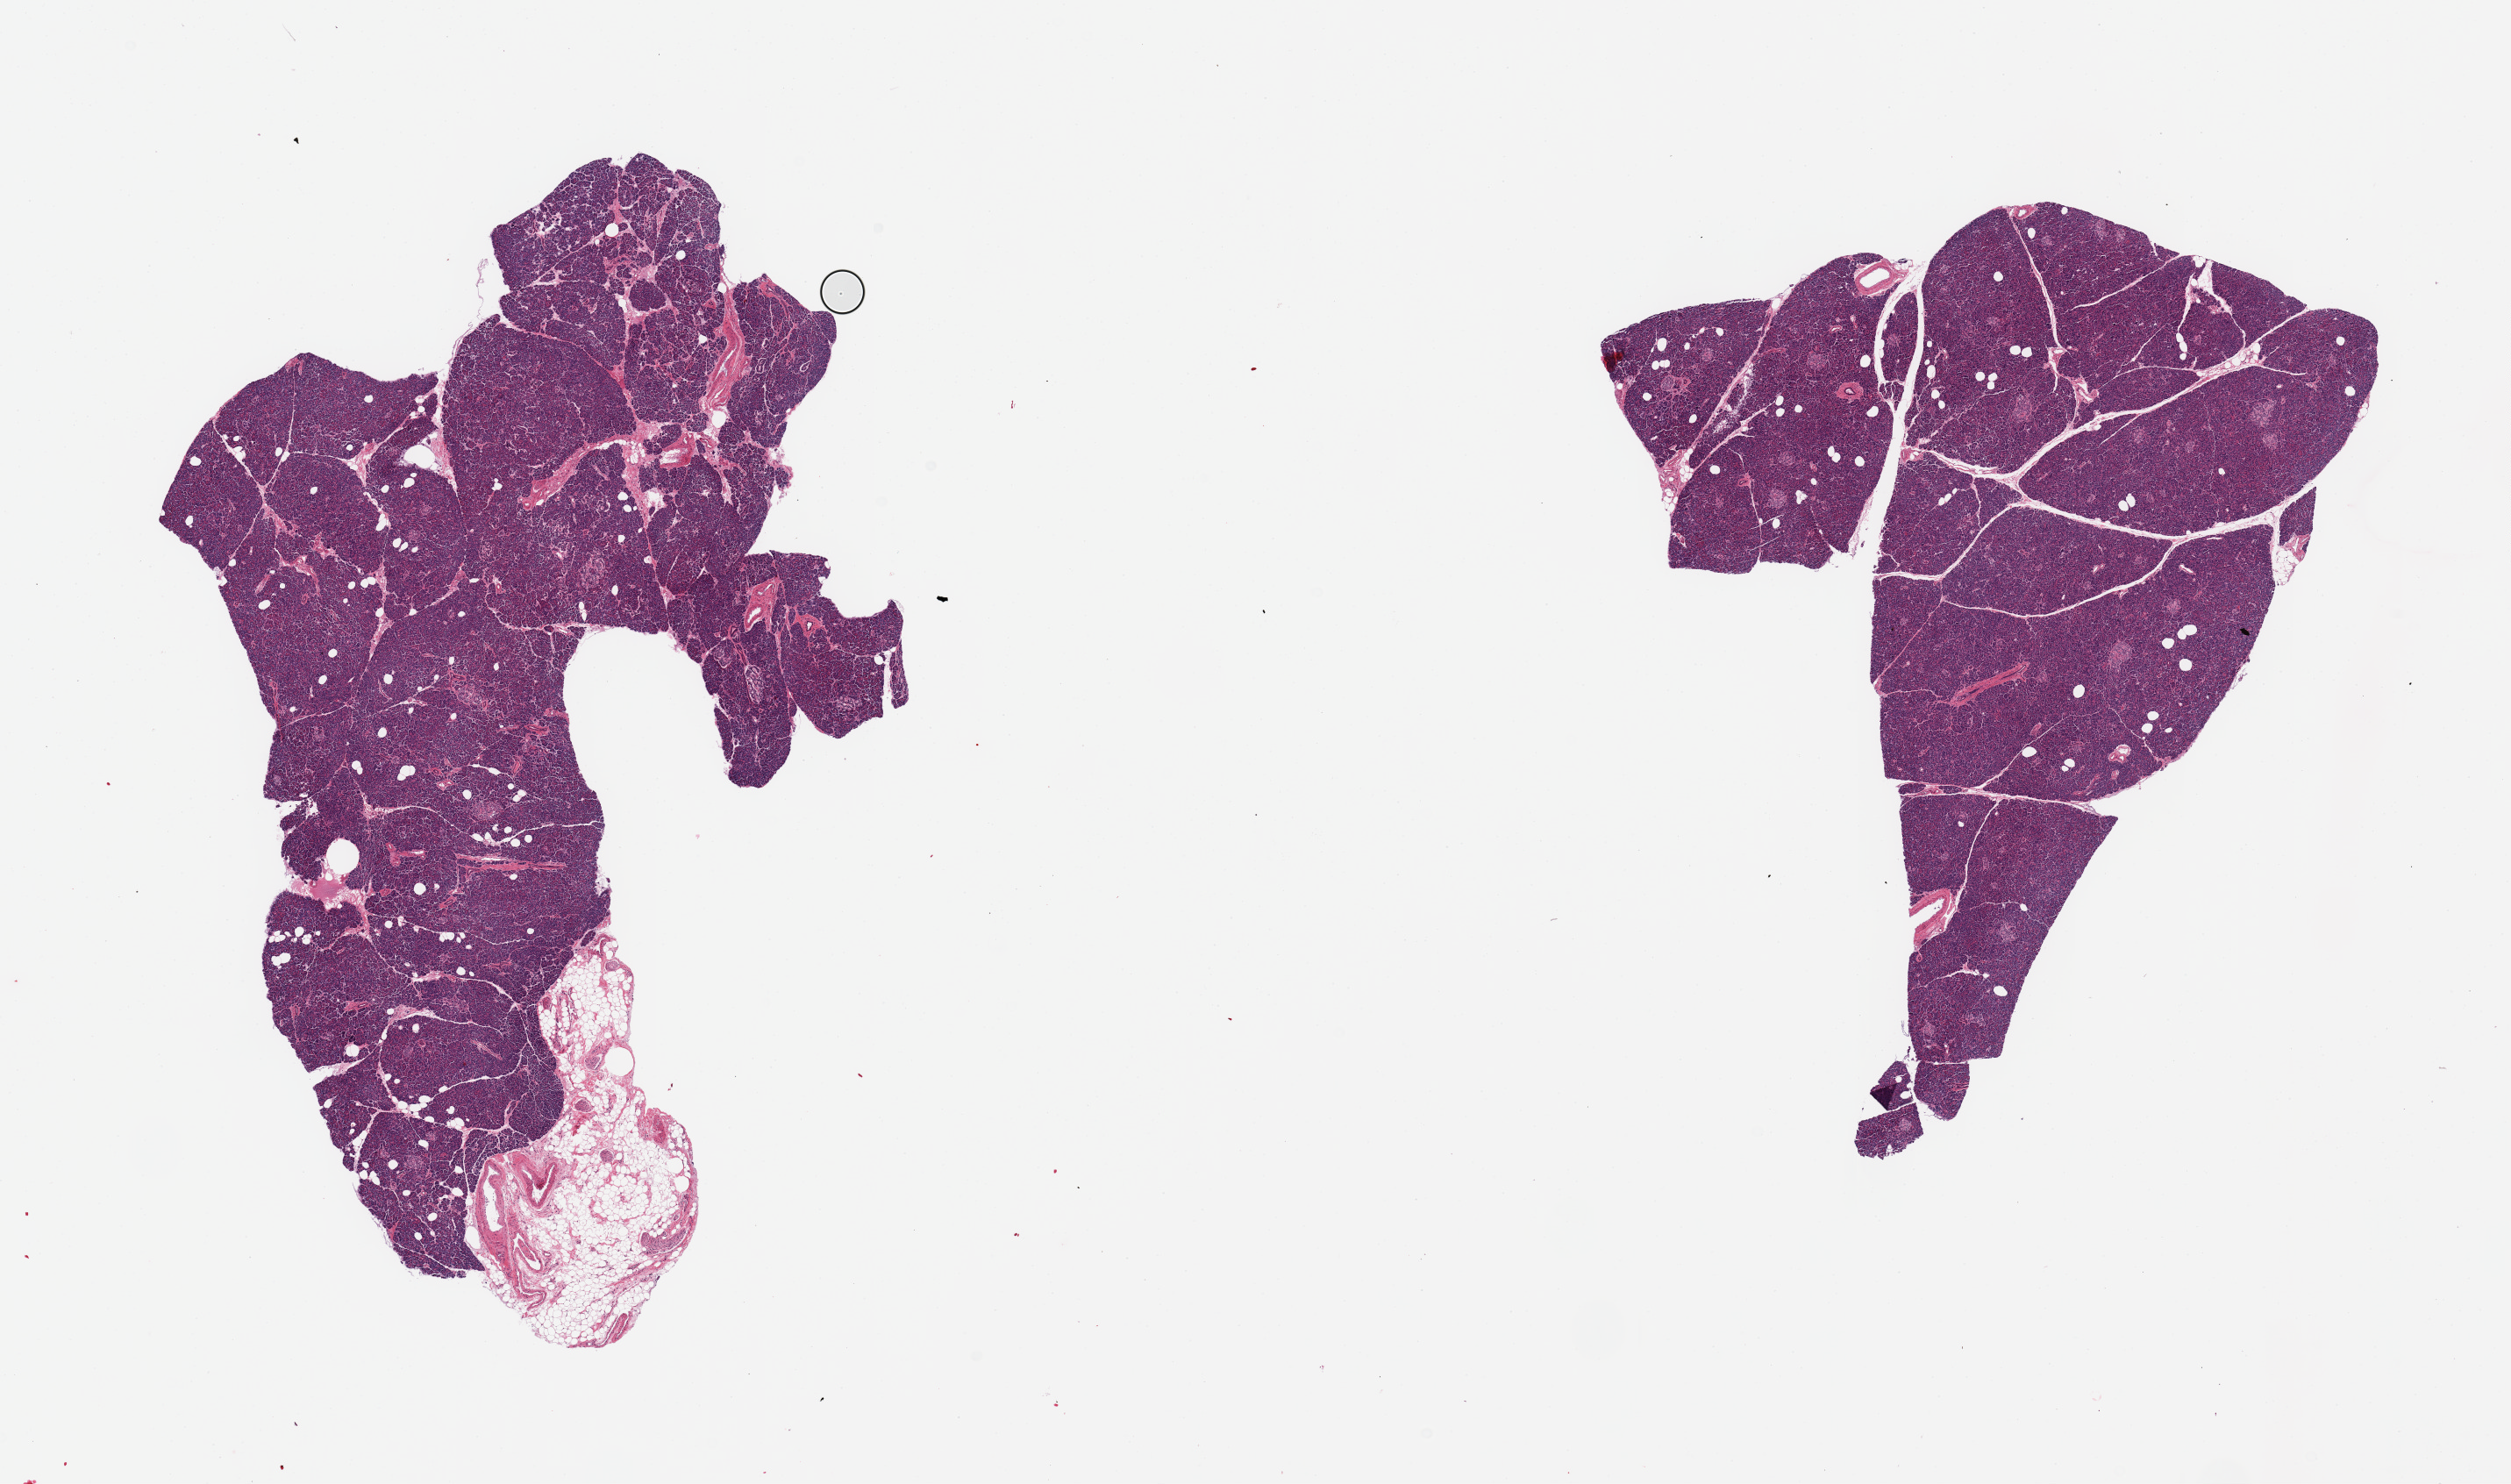
H&E whole-slide image, whole scanned area (about 22.6 x 13.4 mm) shown as a low-resolution overview, PAXgene-fixed, paraffin-embedded tissue, section of pancreas (target tissue), tissue donor sample. Donor sex: male.
* review note (as recorded): 2 pieces; small attachment of fat/nerve/vessels on 1 piece